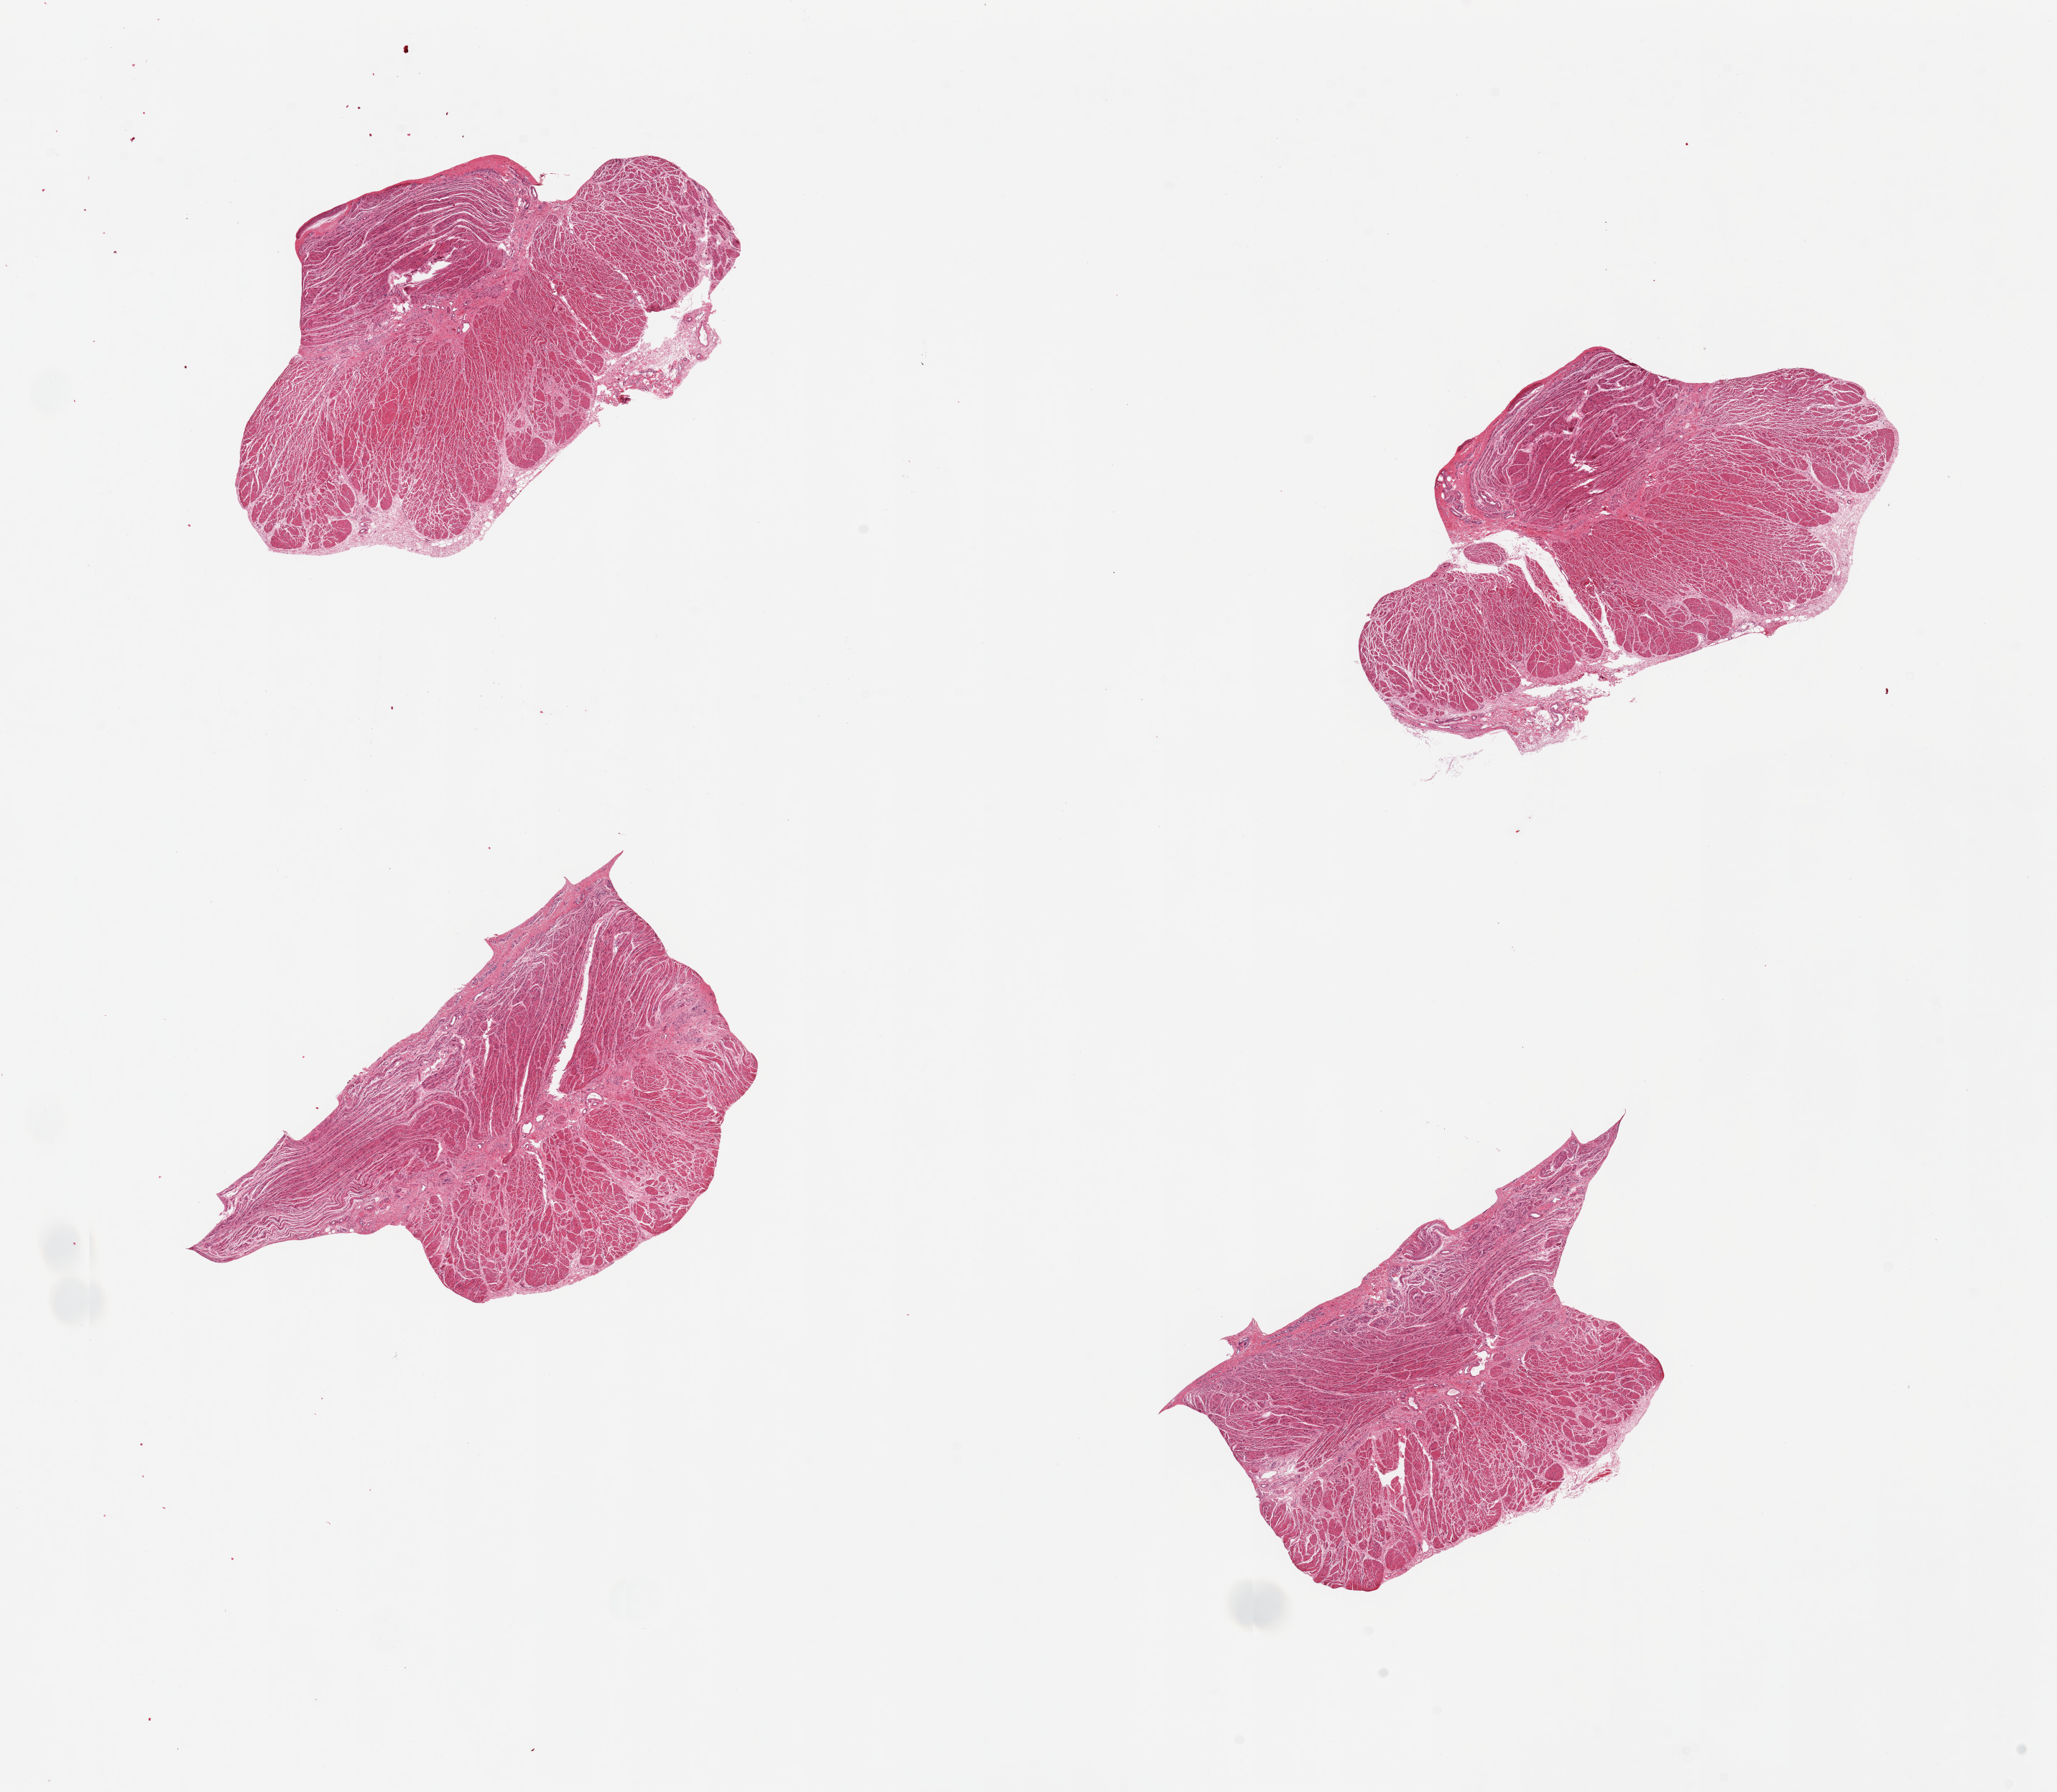
H&E whole-slide image, whole scanned area (about 22.6 x 19.7 mm) shown as a low-resolution overview. PAXgene-fixed paraffin-embedded (PFPE) section. Target tissue: gastroesophageal junction. Tissue donor sample. Male donor.
Reviewer comment on this tissue sample: 4 pieces, all muscularis.